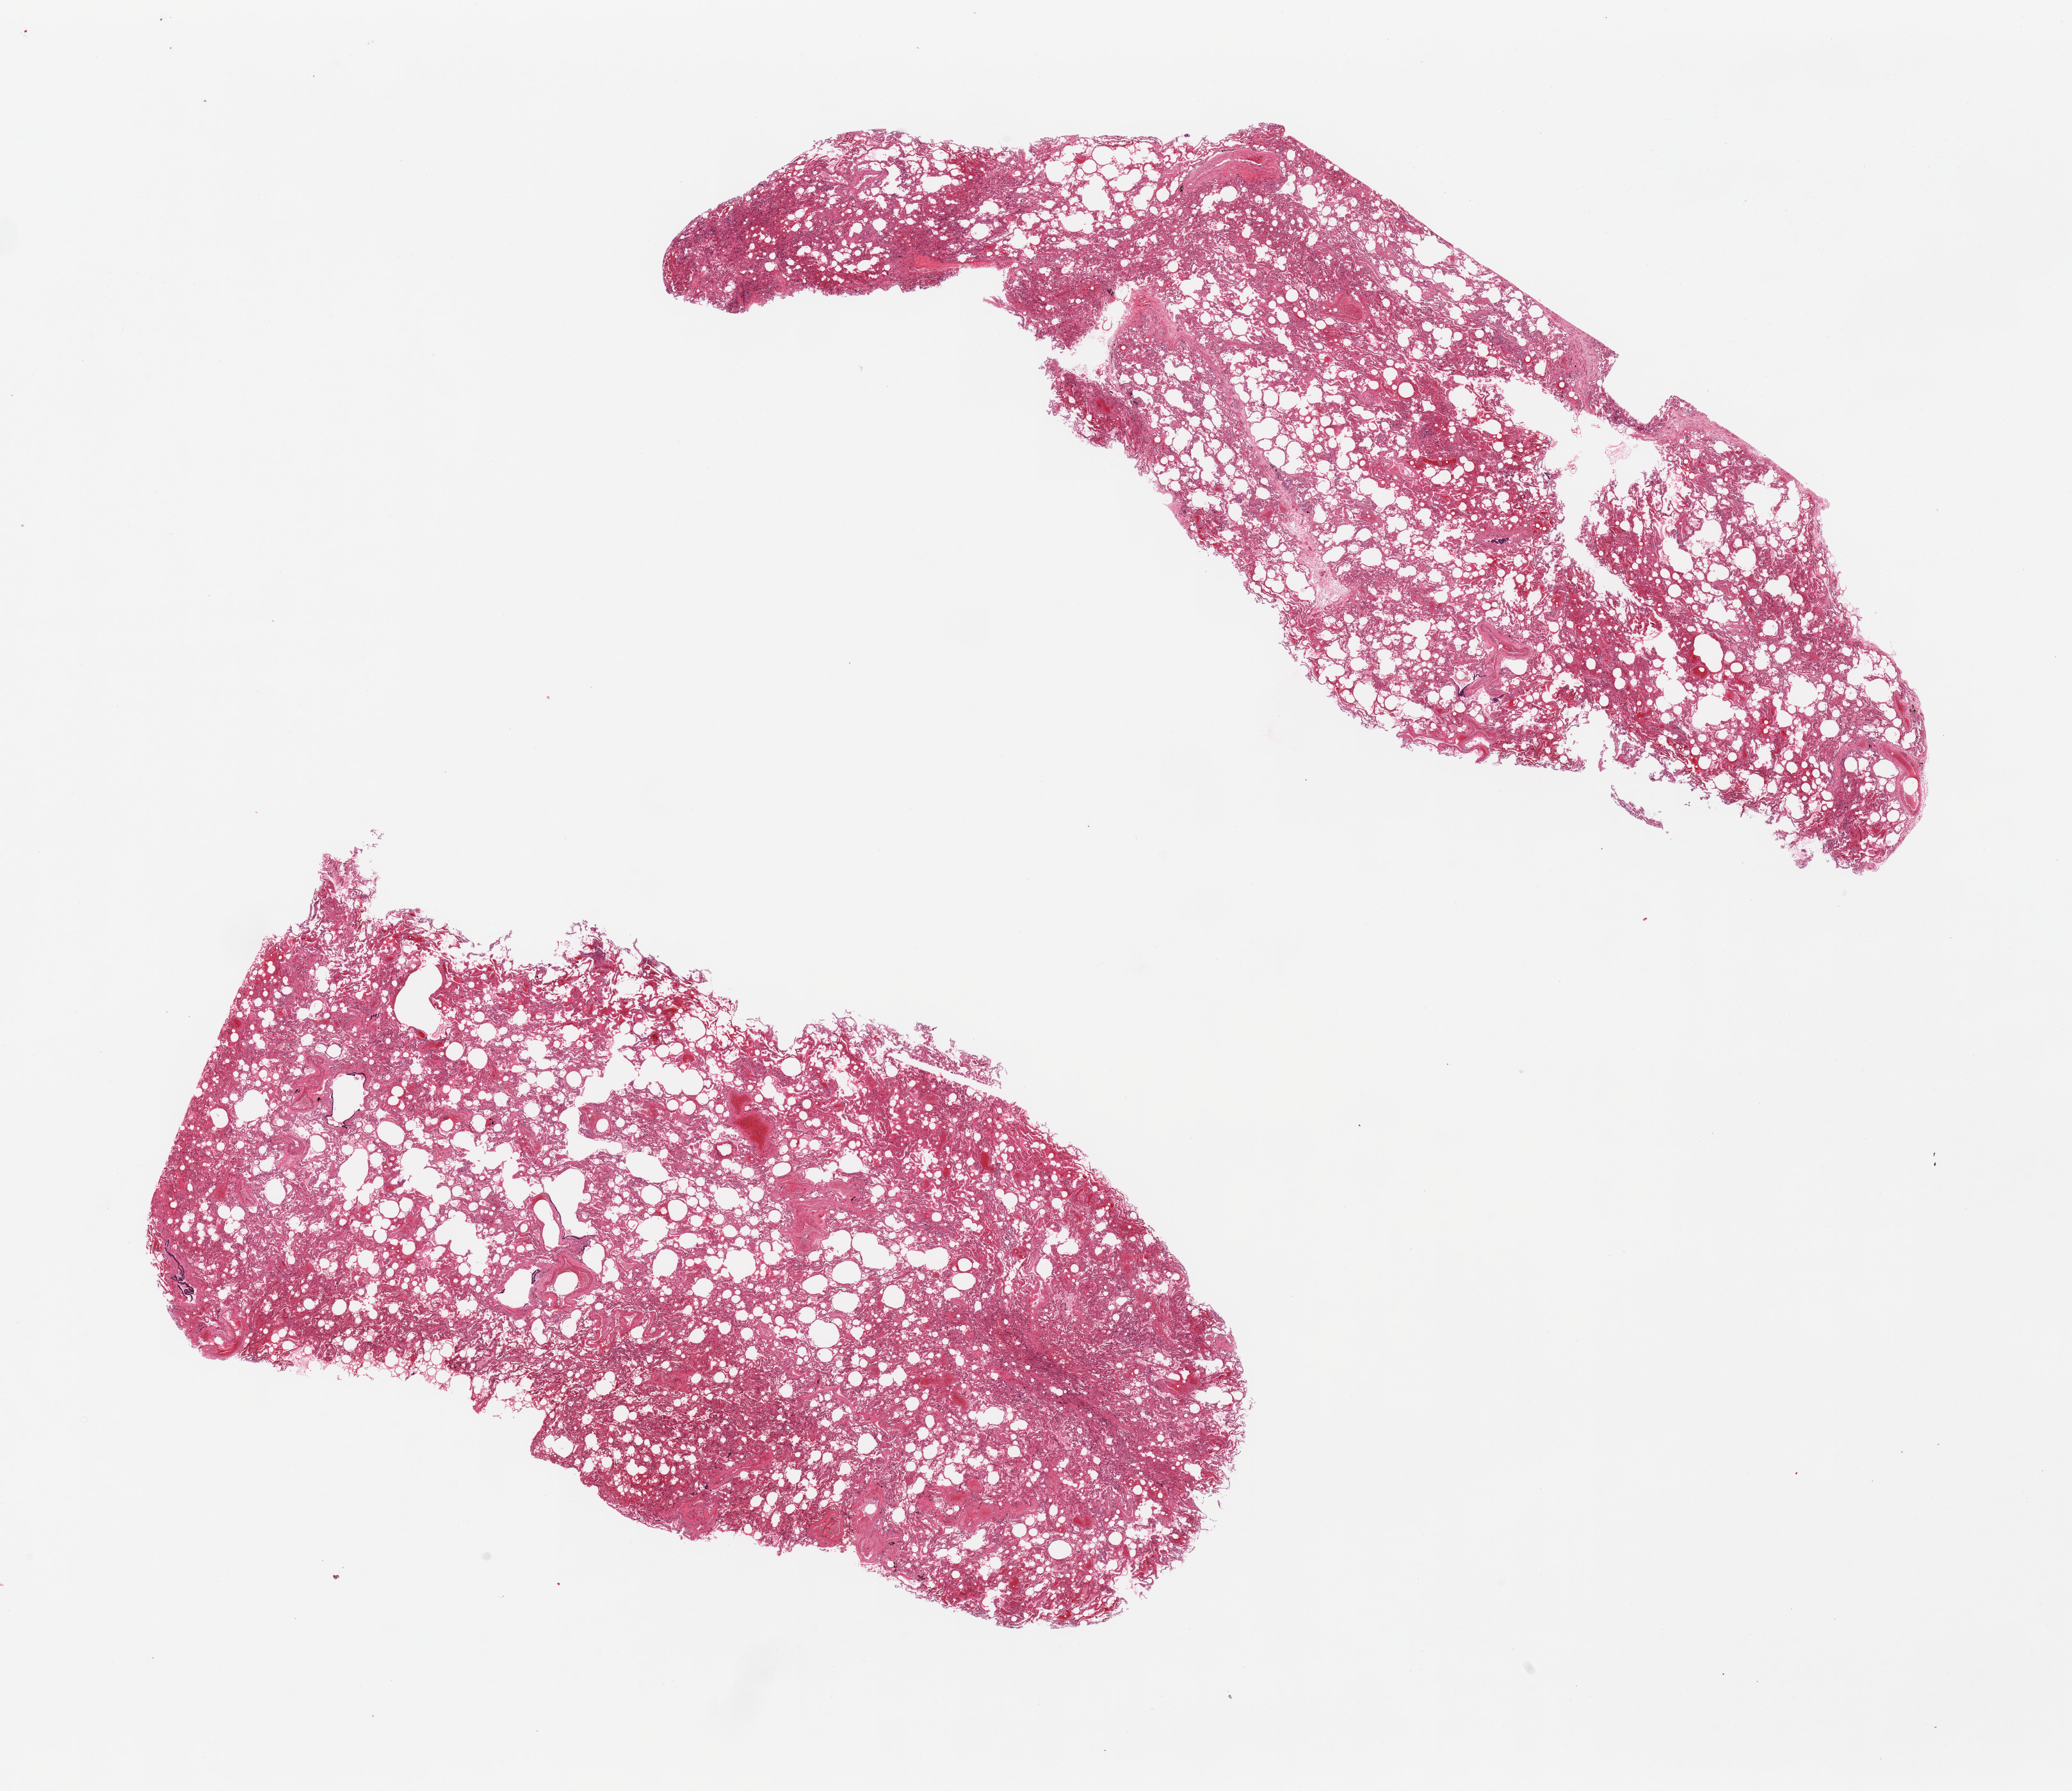
Digitized H&E-stained section — whole scanned area (about 25.6 x 22.1 mm) shown as a low-resolution overview. PAXgene-fixed, paraffin-embedded tissue. Sampled site (target tissue): lung. Tissue donor sample. Male donor.
• reviewer comment on this tissue sample: 2 pieces, moderate congestion